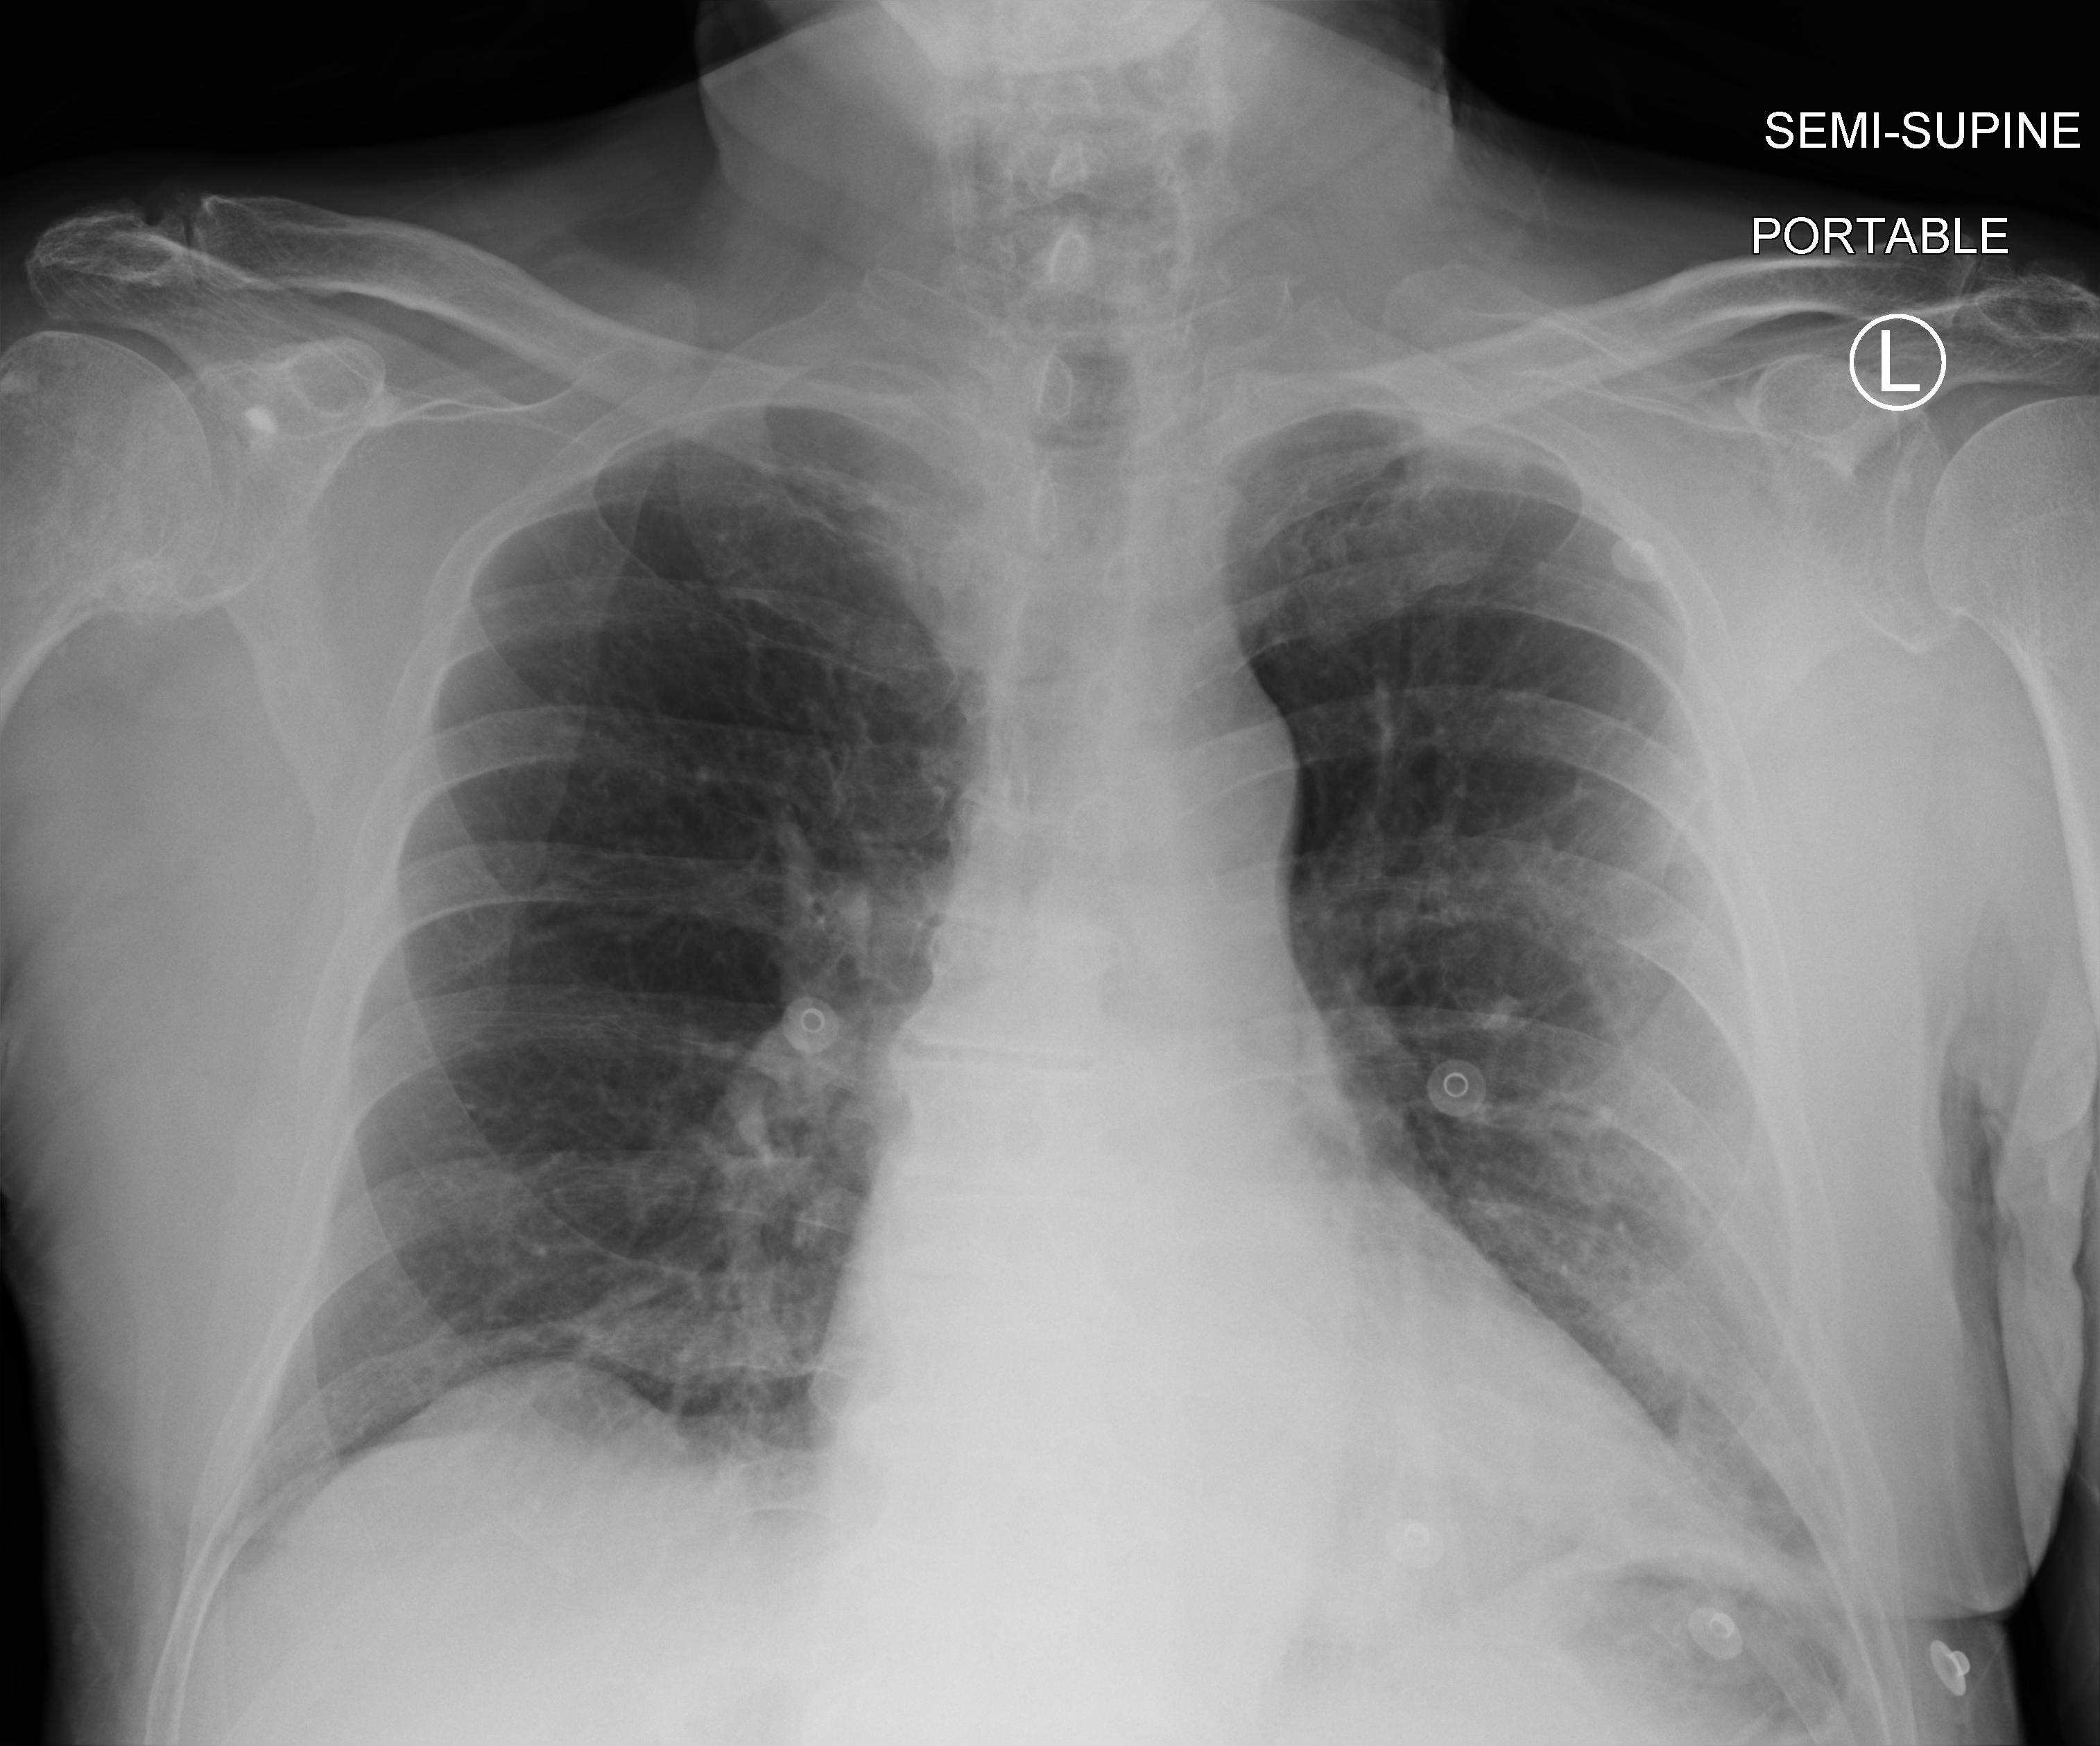
Bedside chest radiograph (computed radiography); anteroposterior (AP) projection. Male patient hospitalised with COVID-19, age 75–90 years.
From the hospital-stay record, not from the radiograph (when in the stay this image was taken is not recorded):
- chronic kidney disease (admission record): no